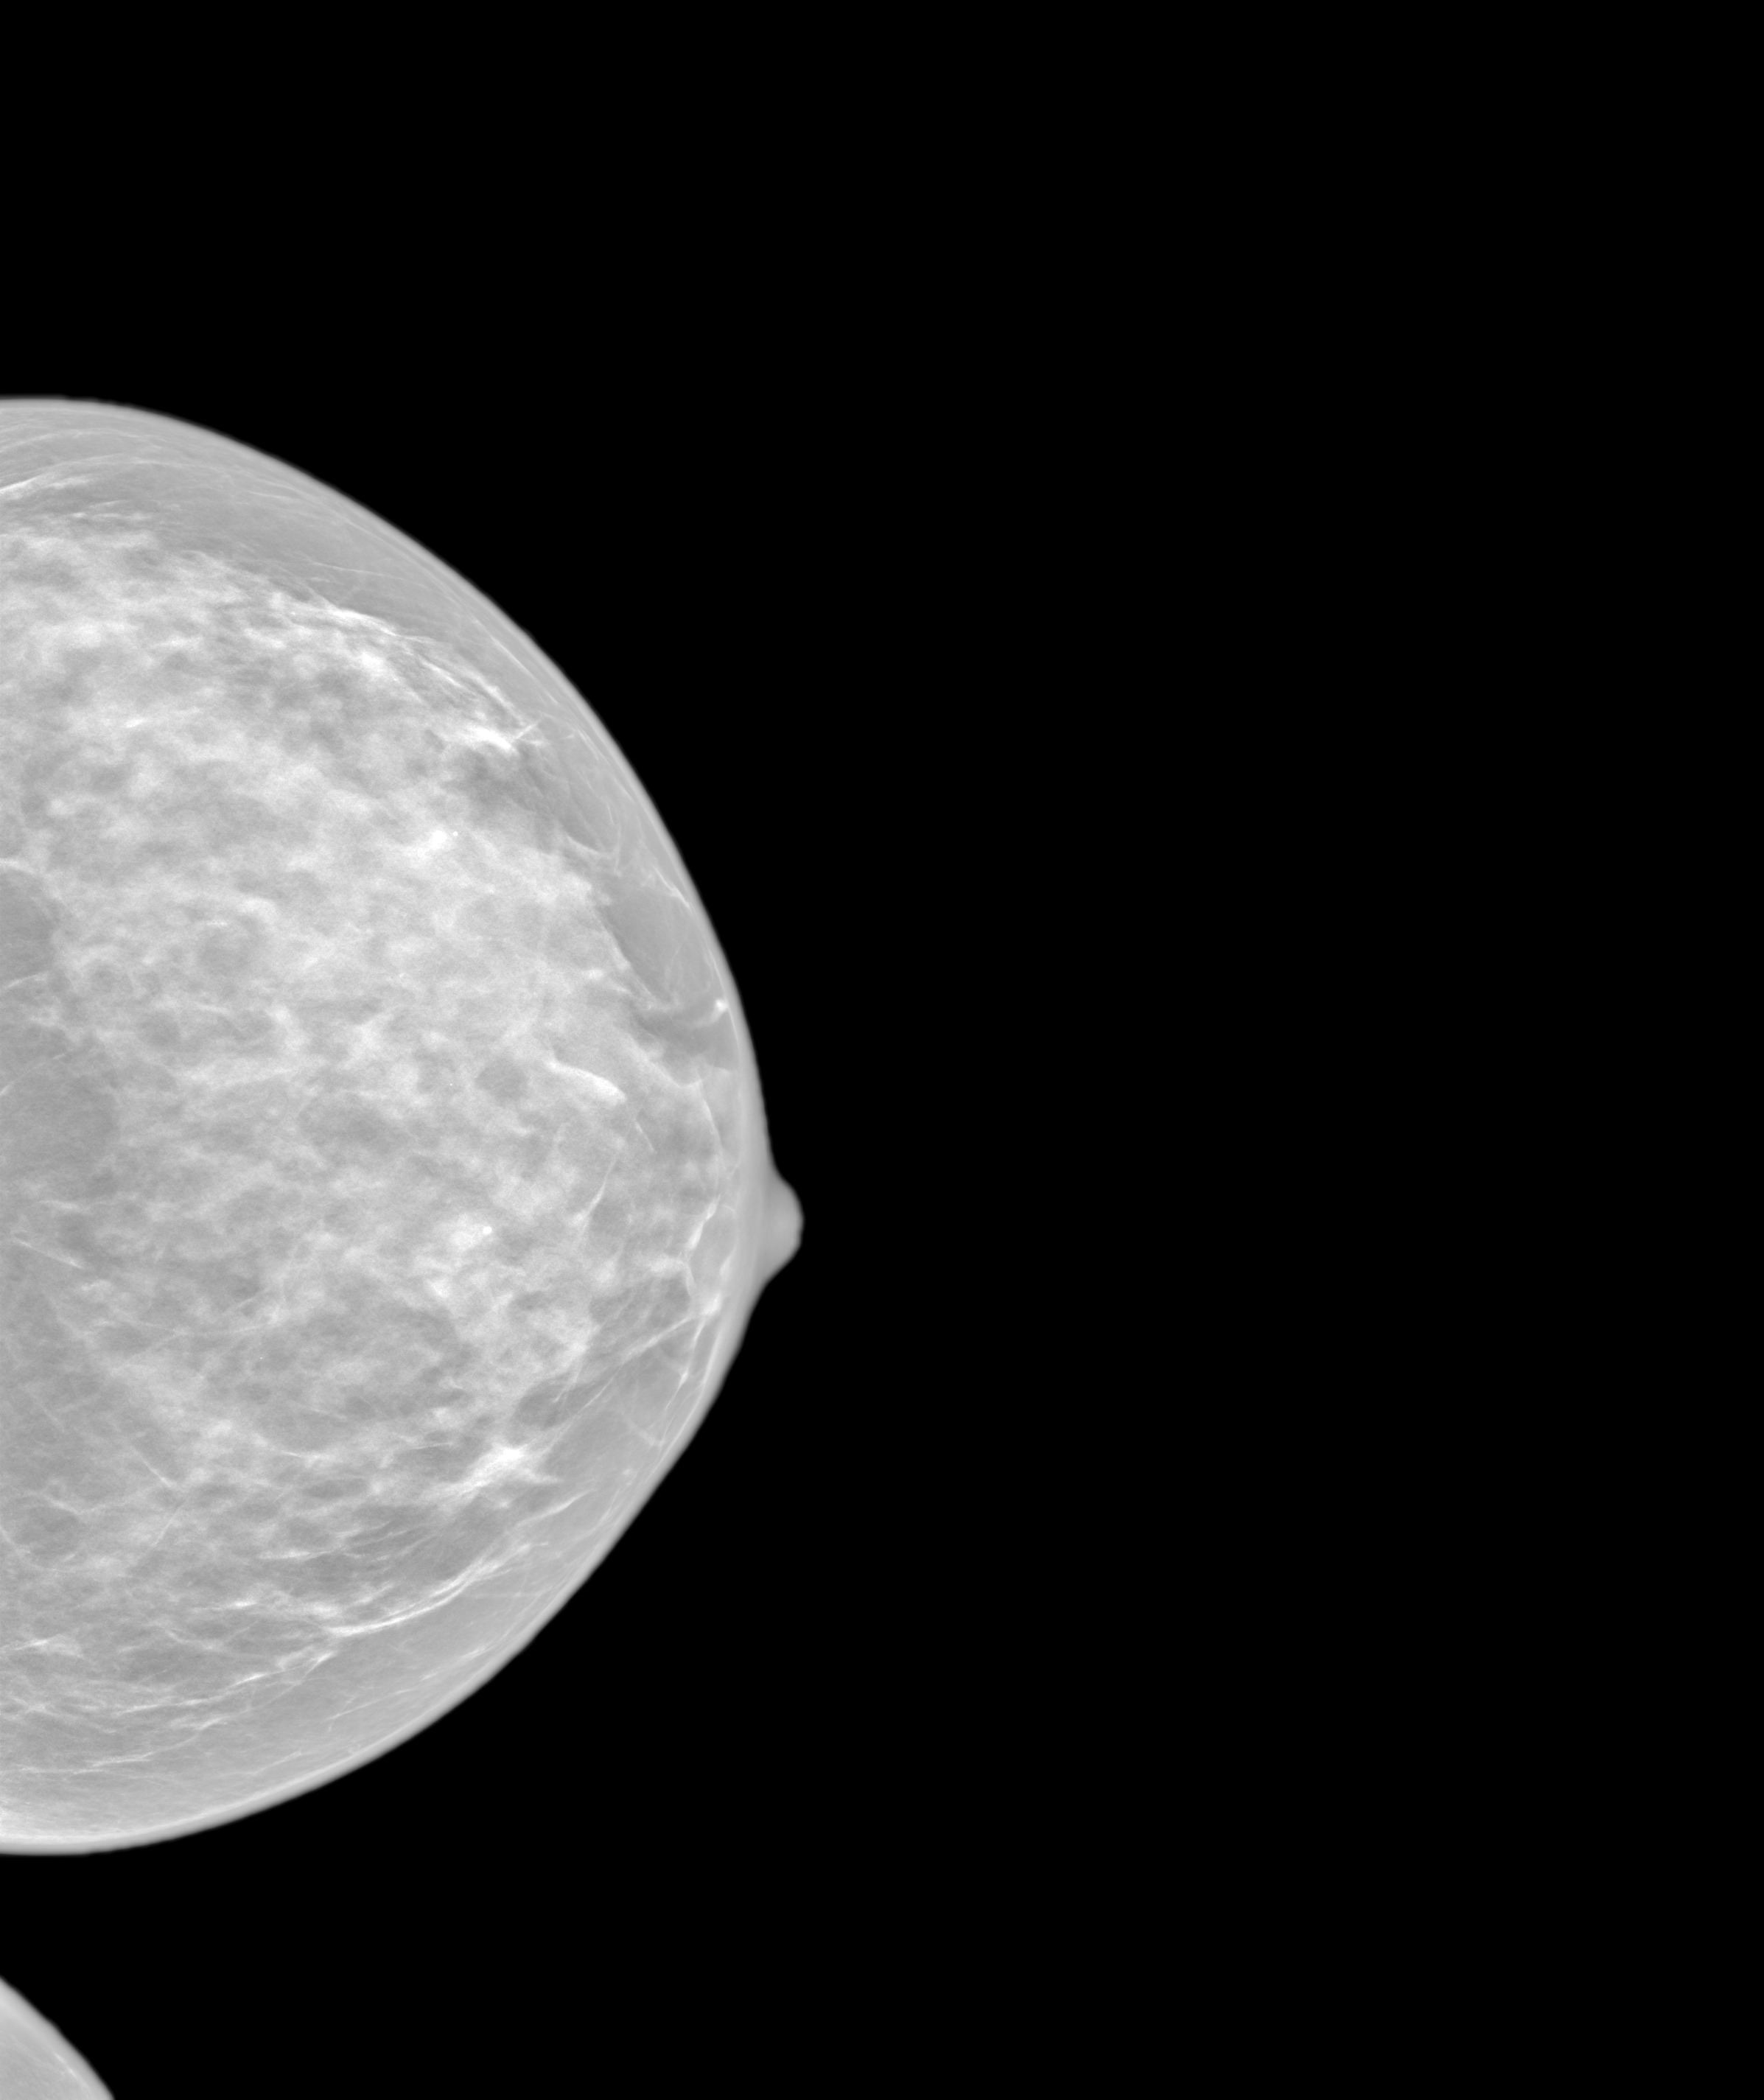
Synthesized 2-D mammogram reconstructed from digital breast tomosynthesis; left breast; CC view; screening examination. Patient aged 42 years (female).
- BI-RADS breast density category at the screening exam (both breasts, scale 1–4): 4
- final BI-RADS category for the screening round (tomosynthesis exam, both breasts): category 1
- recall: no recall after this screen